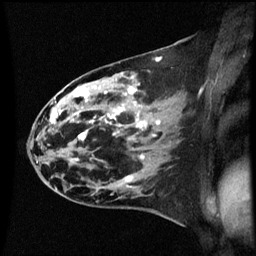
Breast MRI (dynamic contrast-enhanced), one sagittal slice. Slice 33 of 60 in the series (ordered by position). Dynamic contrast-enhanced series, image 2 of 3 at this slice position (ordered by acquisition). 1.5 T. TE 4.2 ms, TR 8.9 ms. 2 mm slice thickness. 256 × 256 image matrix. Patient: female, 44 years. From the clinical record (not read from this slice): setting: breast cancer imaged before/during neoadjuvant chemotherapy; receptor status: HR-positive, HER2-negative.
Annotated regions visible in this slice (semi-automatically segmented with operator editing):
- analysis volume of interest (the breast-tissue region the enhancement analysis was run in; not a lesion): bounding box [x1, y1, x2, y2] px = [43, 78, 153, 189]
- tumour enhancement mask (voxels above the 70 % enhancement threshold inside the analysis volume of interest): [50, 88, 147, 181]